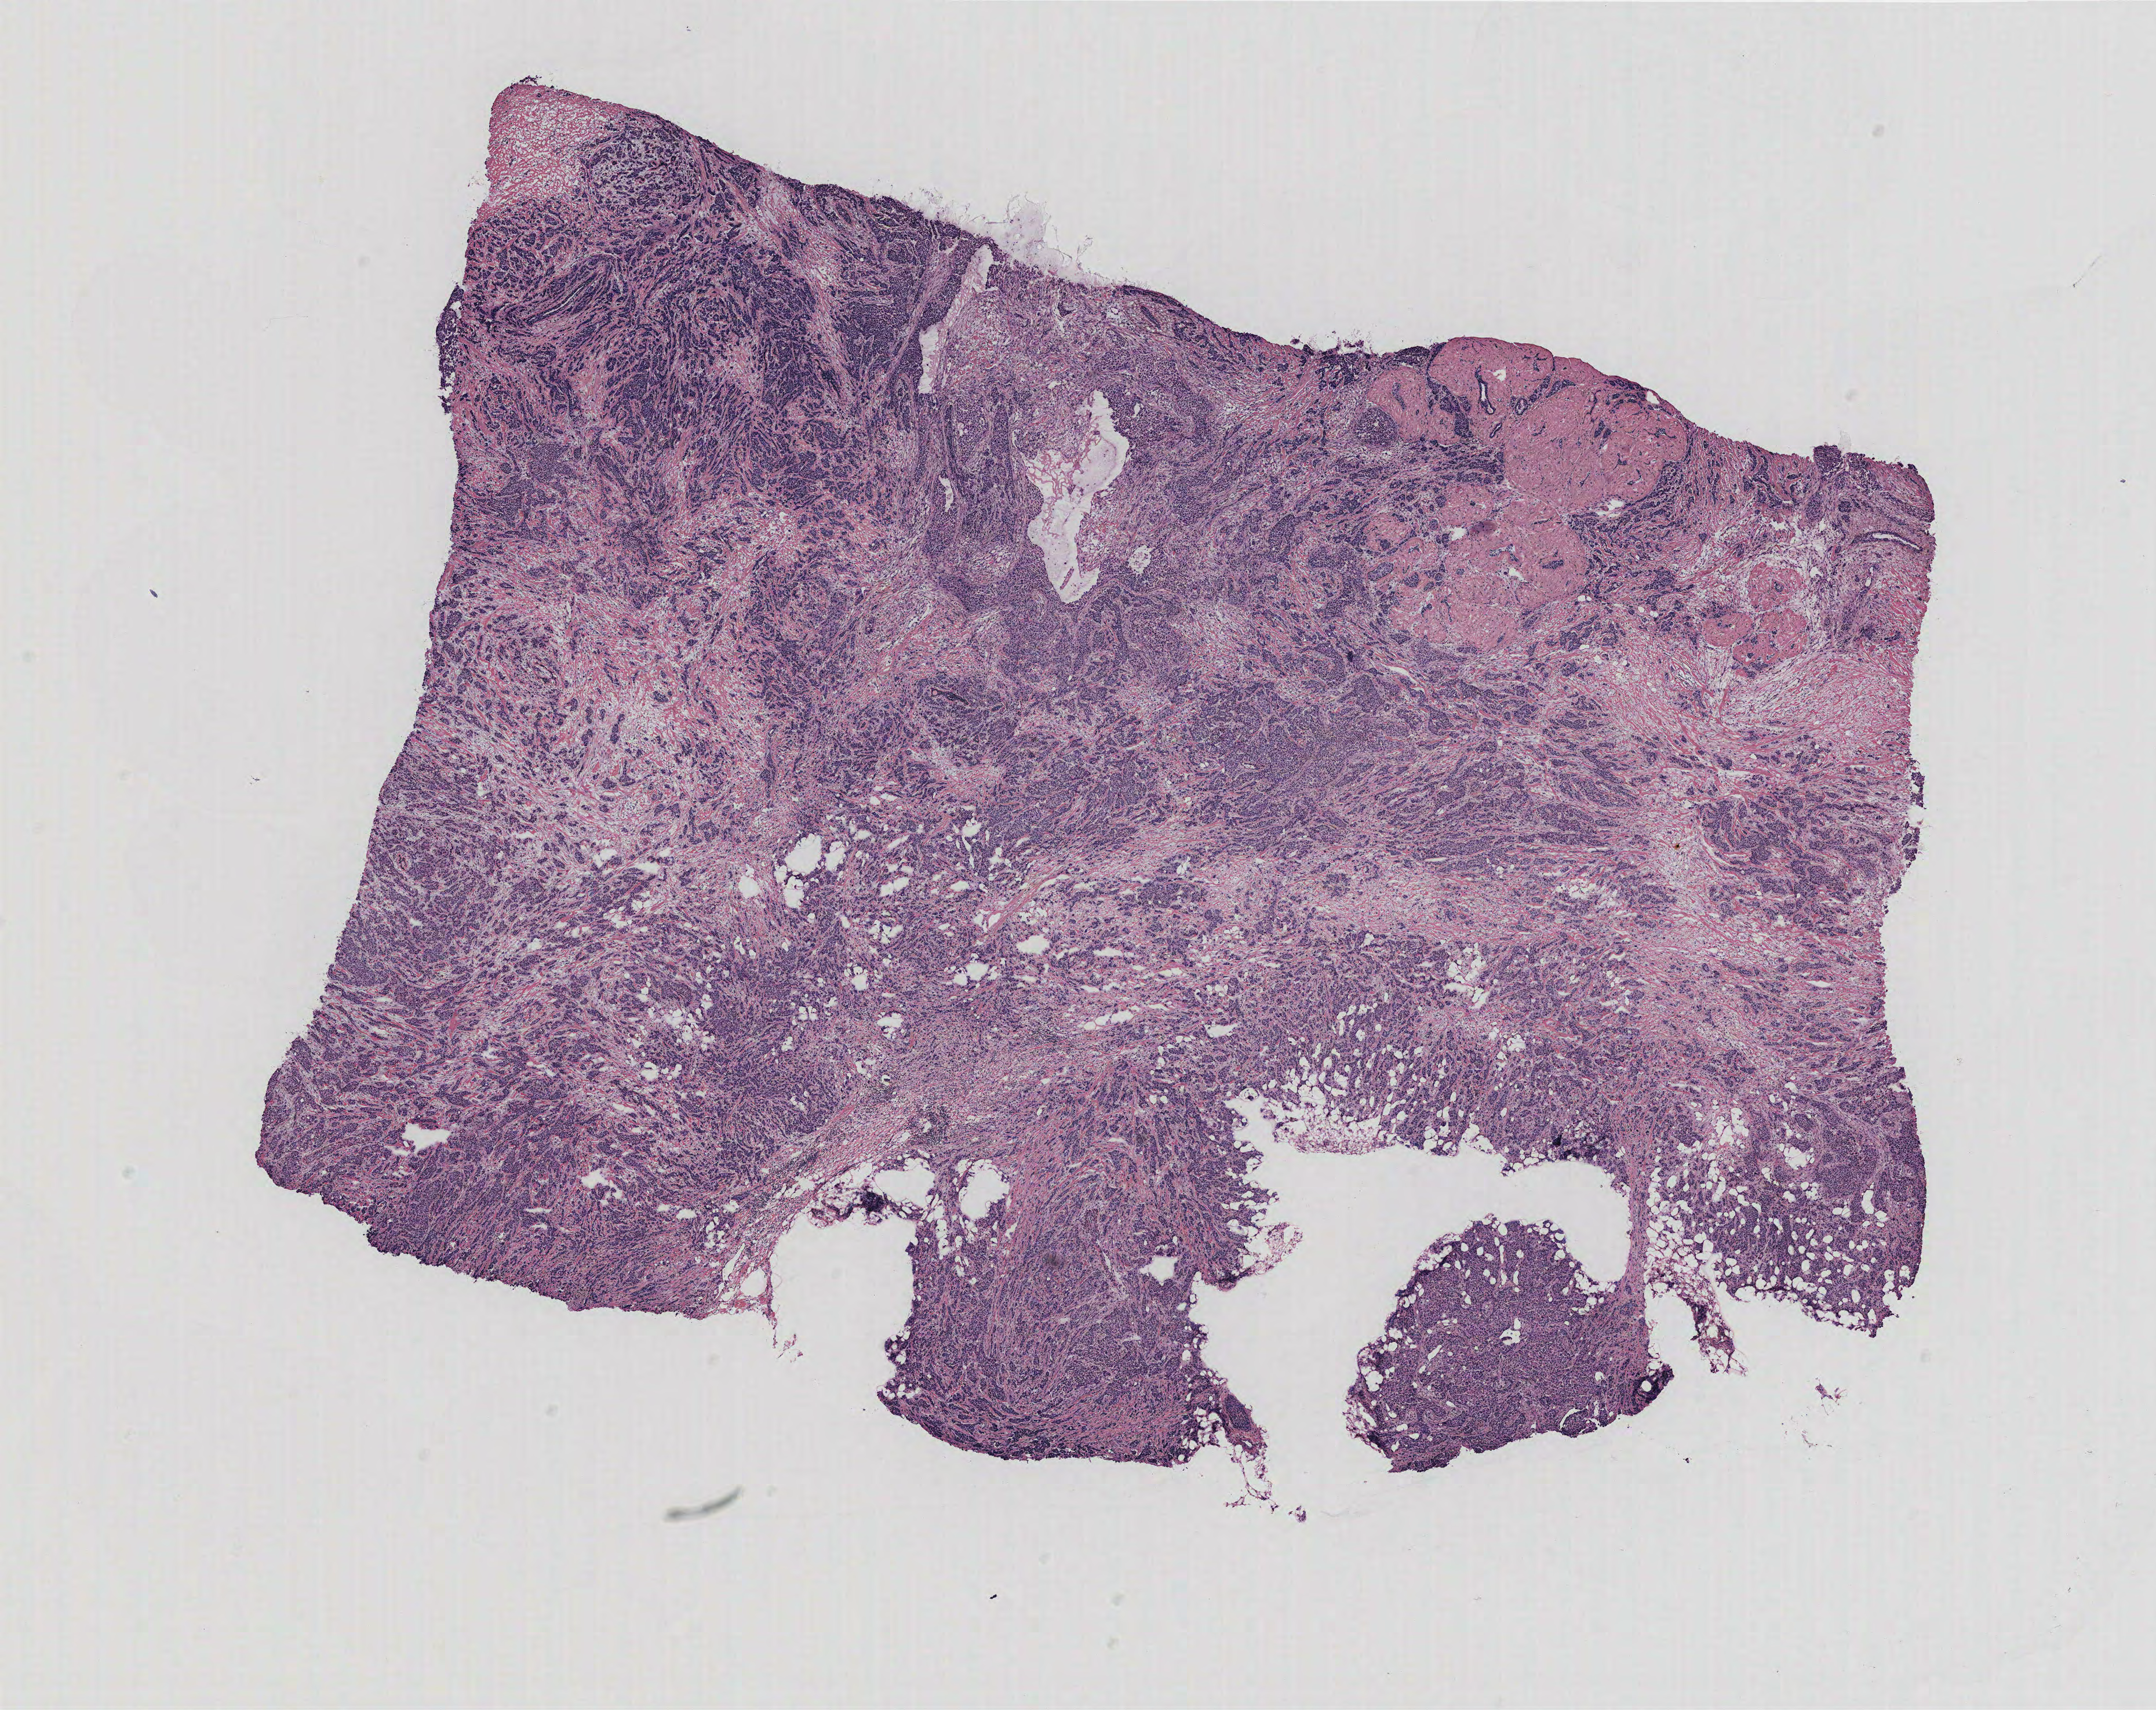
H&E whole-slide image — low-resolution overview of the scanned area, about 14.9 x 11.8 mm, breast, tissue type not recorded. Patient: female, age 38 years.
Patient diagnosis: Infiltrating duct carcinoma, NOS.